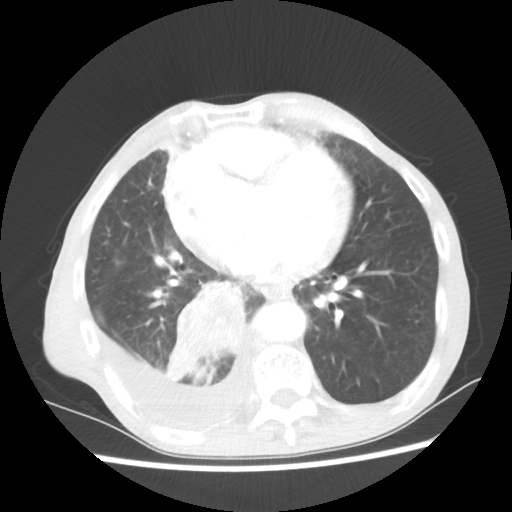
Chest CT, one axial slice. Position 24 of 60 along the scan axis. Reconstruction kernel STANDARD. 80 kVp. Lung window (W 1500 / L -600 HU). 512 × 512 image matrix, field of view 335 × 335 mm. Male patient, age 76 years. From the clinical record (not read from this slice): clinical TNM (as recorded): T3 N3 M1a; histopathological grade: G3.
Outlined on this slice (bounding box drawn by a radiologist):
- lung tumour (recorded histology: squamous cell carcinoma): bounding box <158,280,250,382> (left, top, right, bottom; pixels)